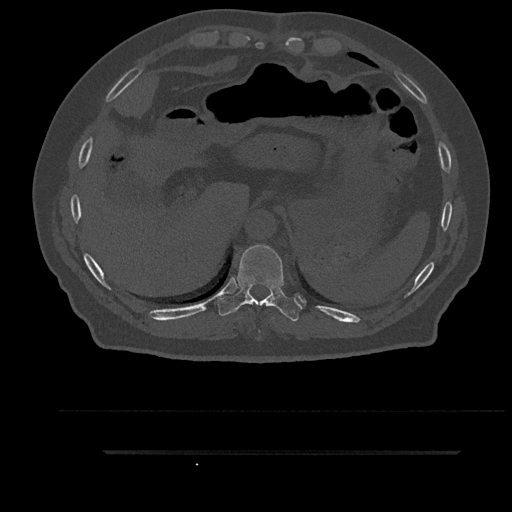
CT including the spine, one axial slice; slice 377 of 797 in the series (ordered by position); reconstruction kernel Br40s/3; bone window (W 1800 / L 400 HU); 0.5 mm slice thickness; 512 × 512 image matrix, field of view 432 × 432 mm. Patient: male, 63 years. Case-level facts recorded for this patient, not image findings: primary cancer: renal; vertebrae with lytic lesions (as recorded): T8.
Outlined on this slice (semi-automatically segmented with operator editing):
- T10 vertebra: box from (x=218, y=245) to (x=303, y=322) px
- T9 vertebra: (x=259, y=303)–(x=265, y=333)